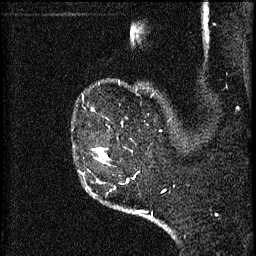
Breast MRI (dynamic contrast-enhanced), one sagittal slice. Position 50 of 60 along the scan axis. 3 images stored at this slice position (order not interpretable as contrast timing). 1.5 T. TE 4.2 ms, TR 8.2 ms. 2 mm slice thickness. 256 × 256 image matrix. Female patient, age 49 years.
Outlined on this slice (semi-automatically segmented with operator editing):
- analysis volume of interest (the breast-tissue region the enhancement analysis was run in; not a lesion): box from (x=95, y=148) to (x=105, y=163) px
- tumour enhancement mask (voxels above the 70 % enhancement threshold inside the analysis volume of interest): (x=96, y=154)–(x=105, y=163)